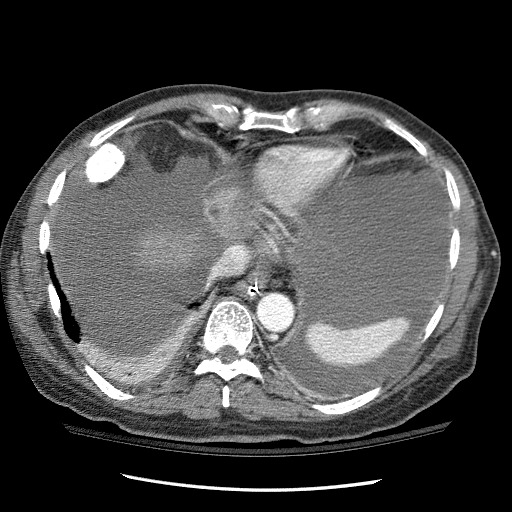
Contrast-enhanced abdominal CT (liver protocol), one axial slice; position 96 of 114 along the scan axis; reconstruction kernel STANDARD; 120 kVp; one of 3 acquisitions stored at this slice position; soft-tissue window (W 400 / L 40 HU); 2.5 mm slice thickness; 512 × 512 image matrix. Case-level facts recorded for this patient, not image findings: diagnosis: hepatocellular carcinoma (patient treated with transarterial chemoembolisation; whether this scan precedes or follows treatment is not stated here); TNM stage (as recorded): Stage-I; Child-Pugh class: C.
Structures marked on this image (semi-automatically segmented with operator editing):
- liver parenchyma outside the tumour (the mass and vessels are separate outlines, so this box may not span the whole liver): bounding box (x1, y1, x2, y2) in pixels: (134, 204, 270, 272)
- mass: (203, 188, 256, 238)